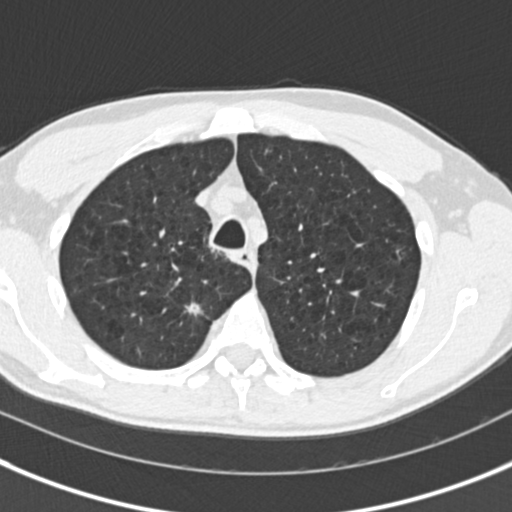
Low-dose screening chest CT, one axial slice; lung window (W 1500 / L -600 HU); 2 mm slice thickness; 512 × 512 image matrix, field of view 306 × 306 mm.
Structures marked on this image (manually delineated by an expert):
- lesion 2 (tumor, upper lobe of right lung): bounding box [x1, y1, x2, y2] px = [185, 302, 203, 316]